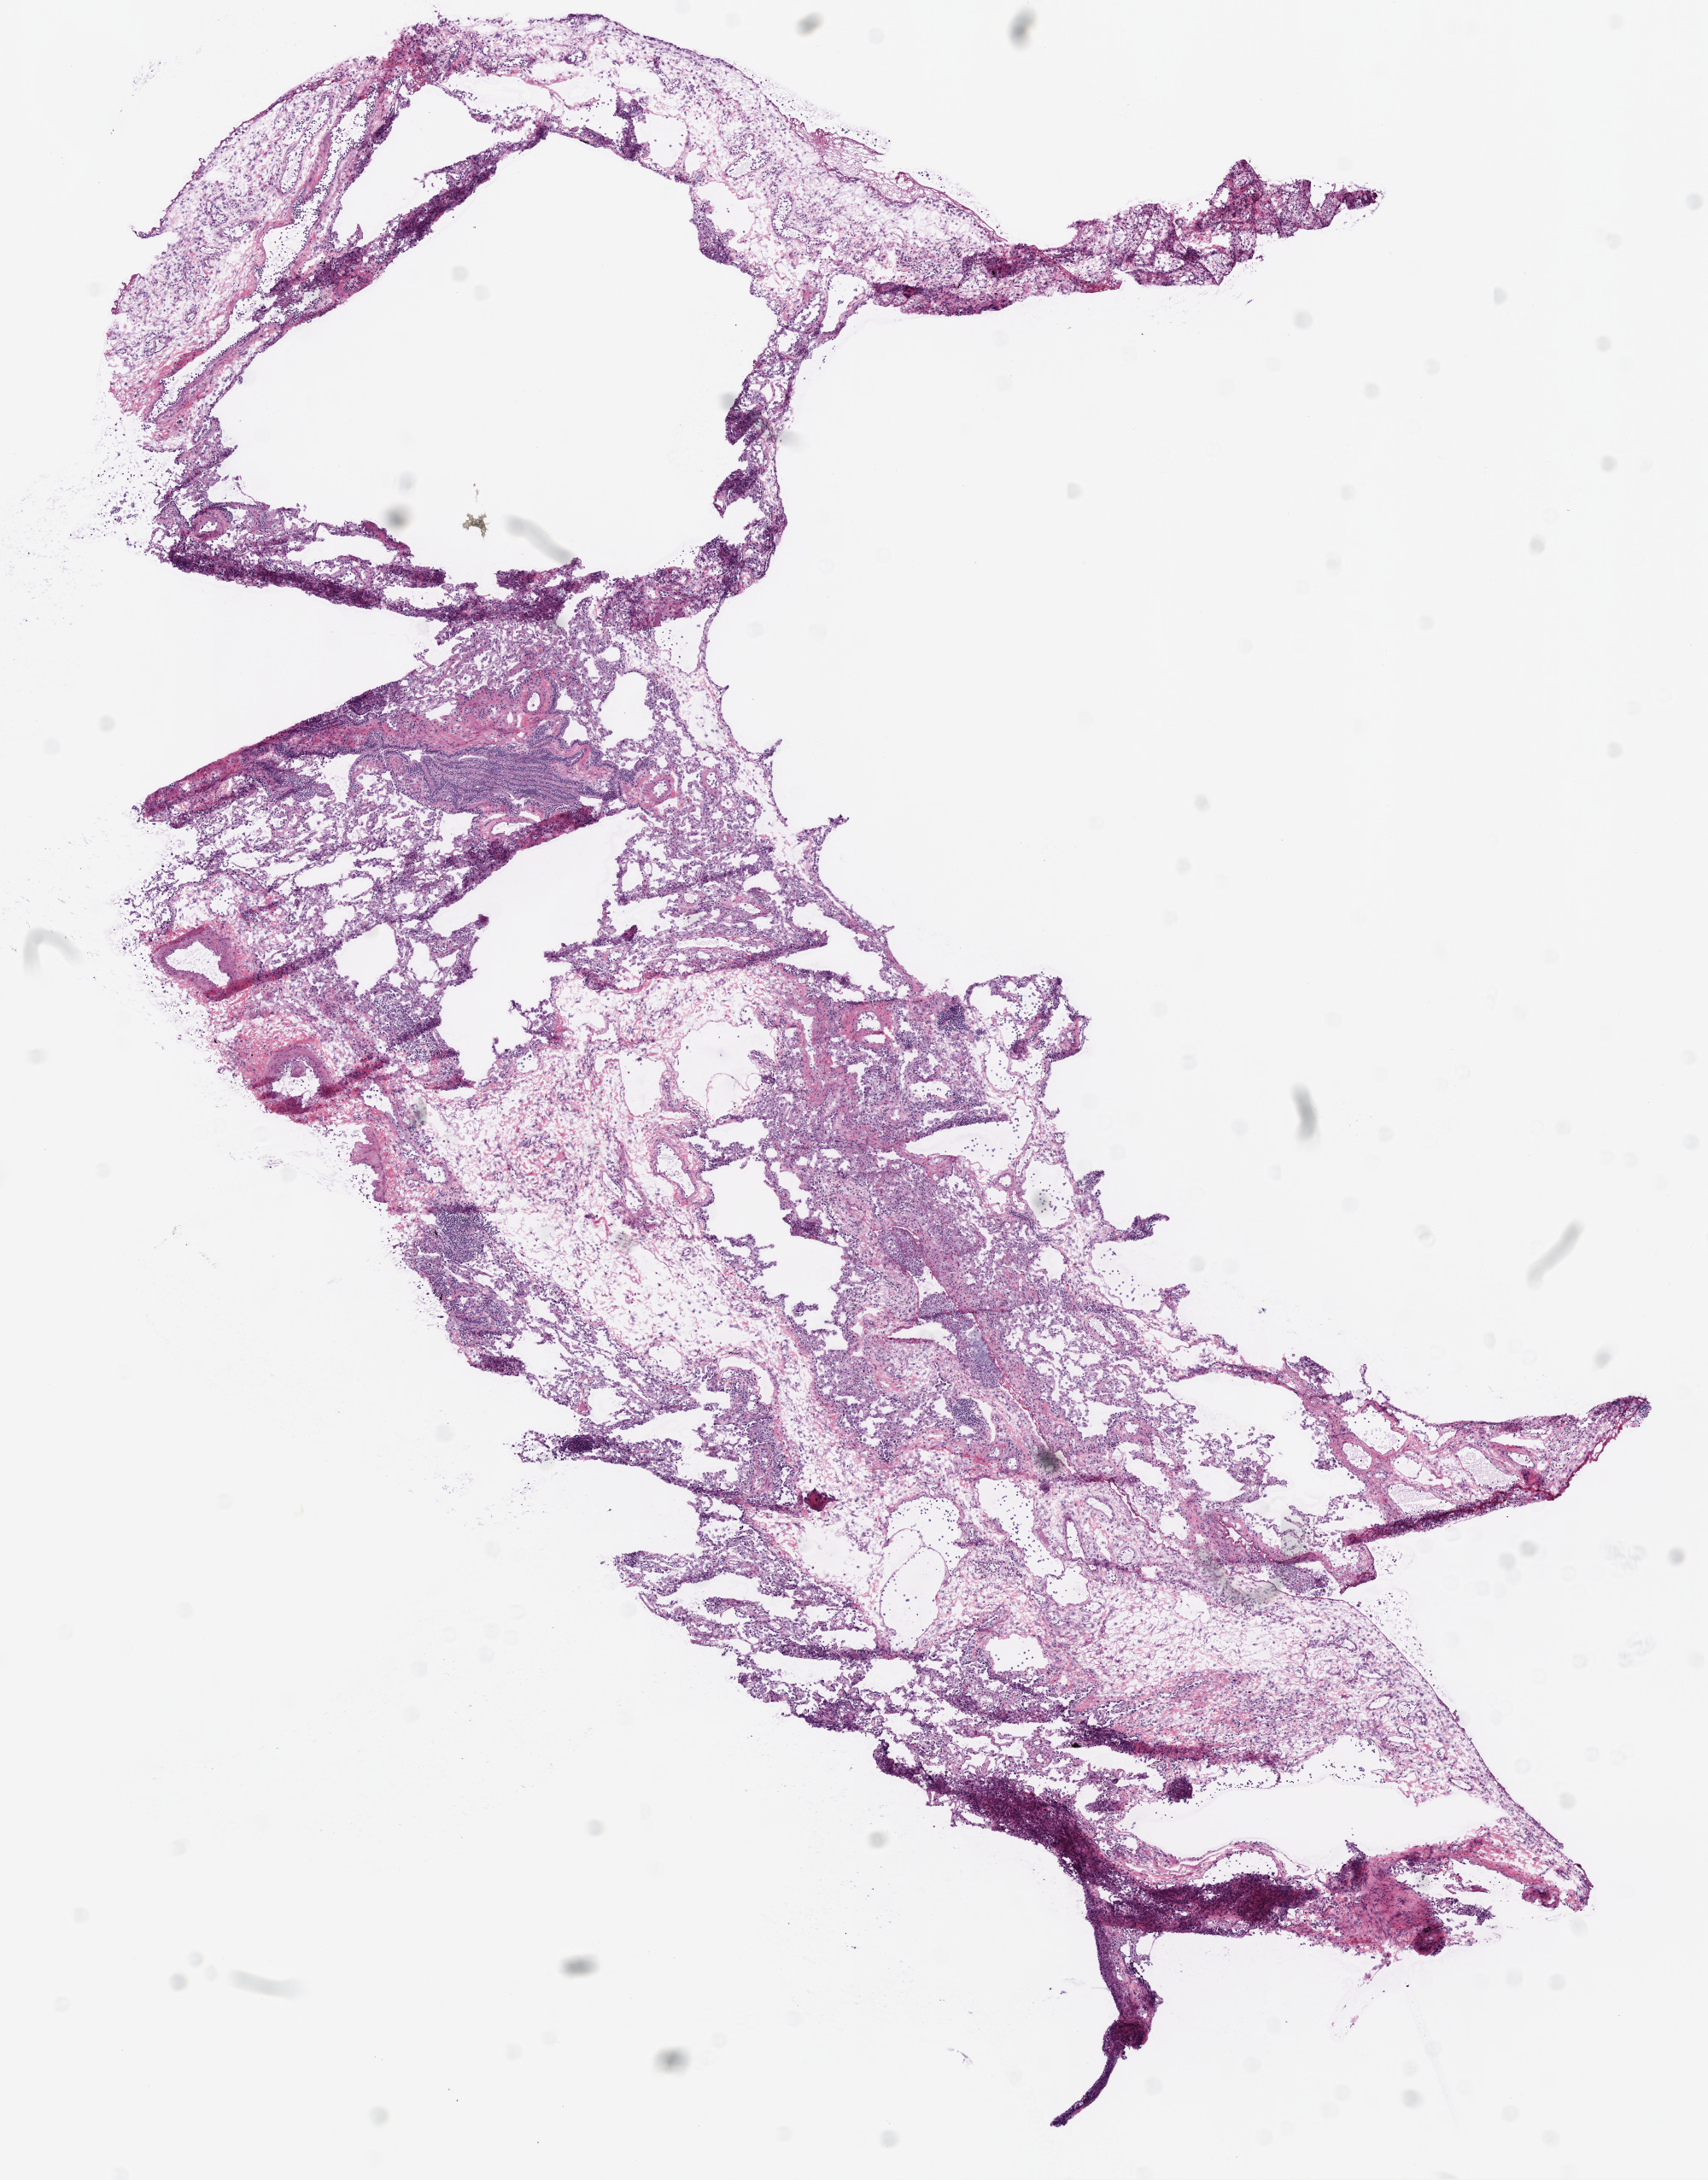
Digitized H&E tissue section (whole slide) — shown as a low-resolution overview of the whole scanned area (about 8.0 x 10.2 mm, slide scanned at 20x); frozen section; lung, solid tissue normal (non-tumour tissue) sample. Male, age 67 years at initial diagnosis.
This section: solid tissue normal (non-tumour) sample from the same patient. Patient diagnosis: Squamous cell carcinoma, NOS.